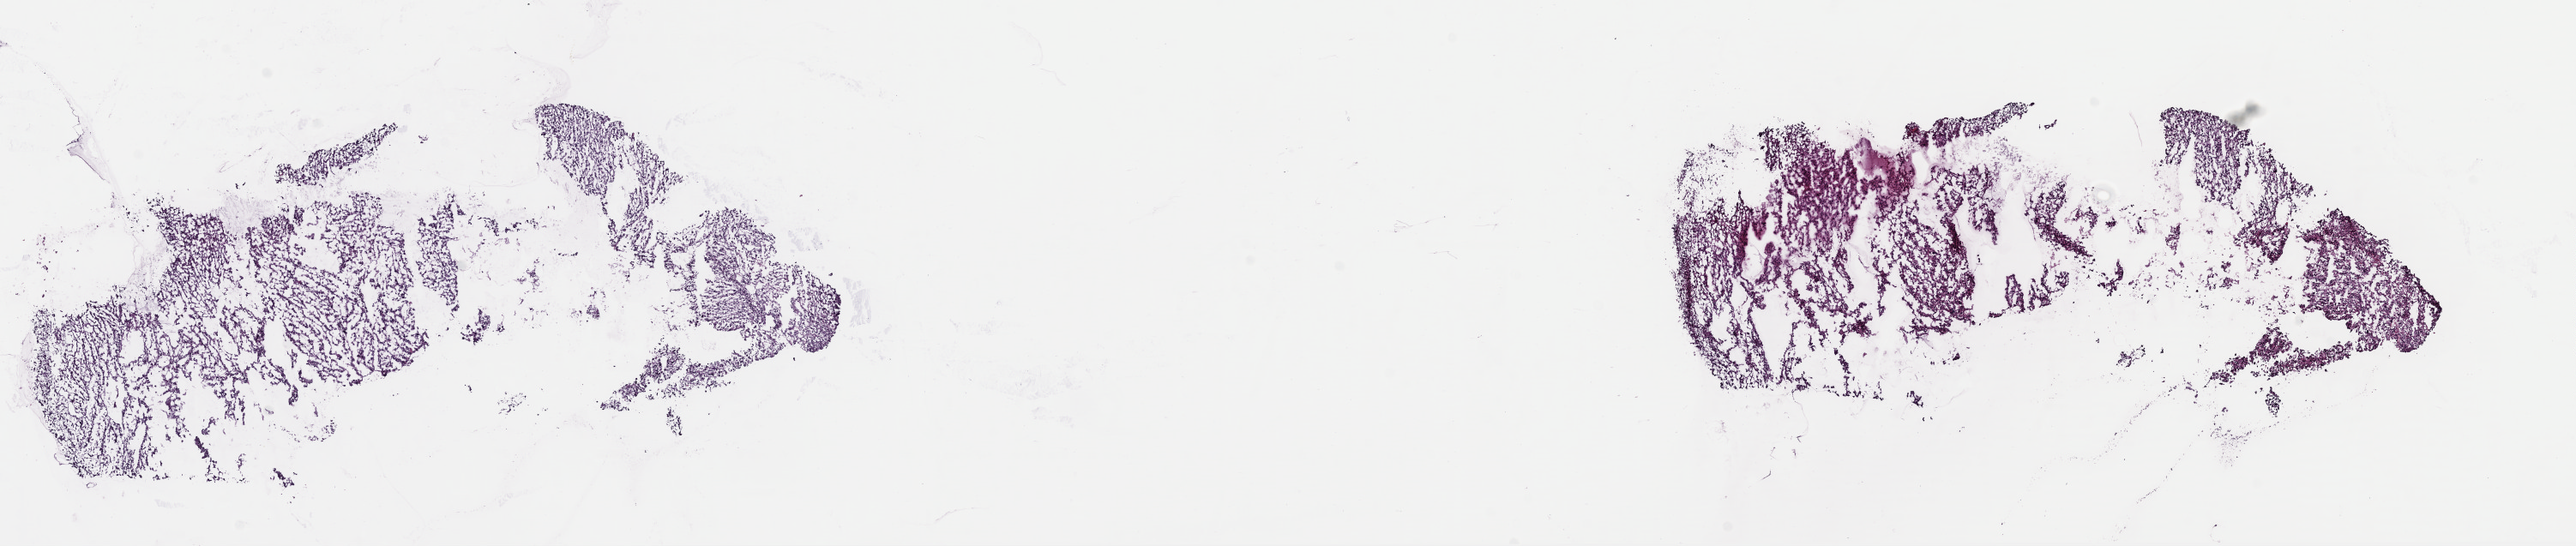
H&E whole-slide image, whole scanned area (about 23.6 x 5.0 mm) shown as a low-resolution overview, frozen section from the top of the tissue portion, connective, subcutaneous and other soft tissues, primary tumour sample. Patient: male, age at initial diagnosis 73 years. Pathologist review of this section (percent, as recorded): tumour cells 90%, tumour nuclei 100%, normal cells 0%, stromal cells 10%, necrosis 0%. Inflammatory infiltration, as recorded: lymphocyte infiltration 0%, monocyte infiltration 0%, neutrophil infiltration 0%.
Diagnosis: Leiomyosarcoma, NOS (connective, subcutaneous and other soft tissues, NOS).